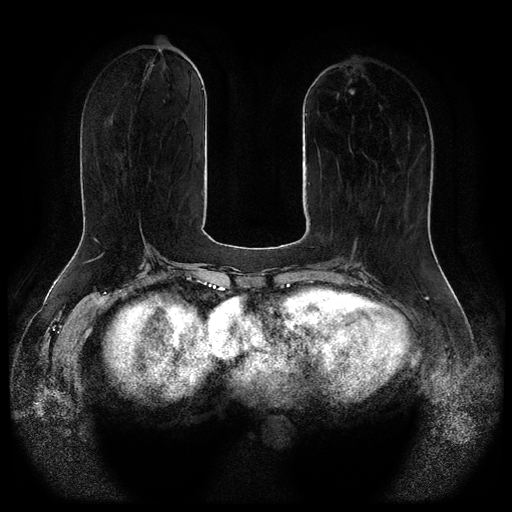
Breast MRI (dynamic contrast-enhanced, multi-phase), one axial slice; position 33 of 116 along the scan axis; dynamic contrast-enhanced series, time point 2 of 5 at this slice position (early post-contrast); 1.5 T; TE 2.6 ms, TR 5.3 ms; 2.1 mm slice thickness; 512 × 512 image matrix. Female patient, age 65 years.
Outlined on this slice (semi-automatic segmentation, software-assisted and operator-edited):
- breast lesion (labelled benign in the annotation): bounding box [x1, y1, x2, y2] px = [349, 89, 355, 95]